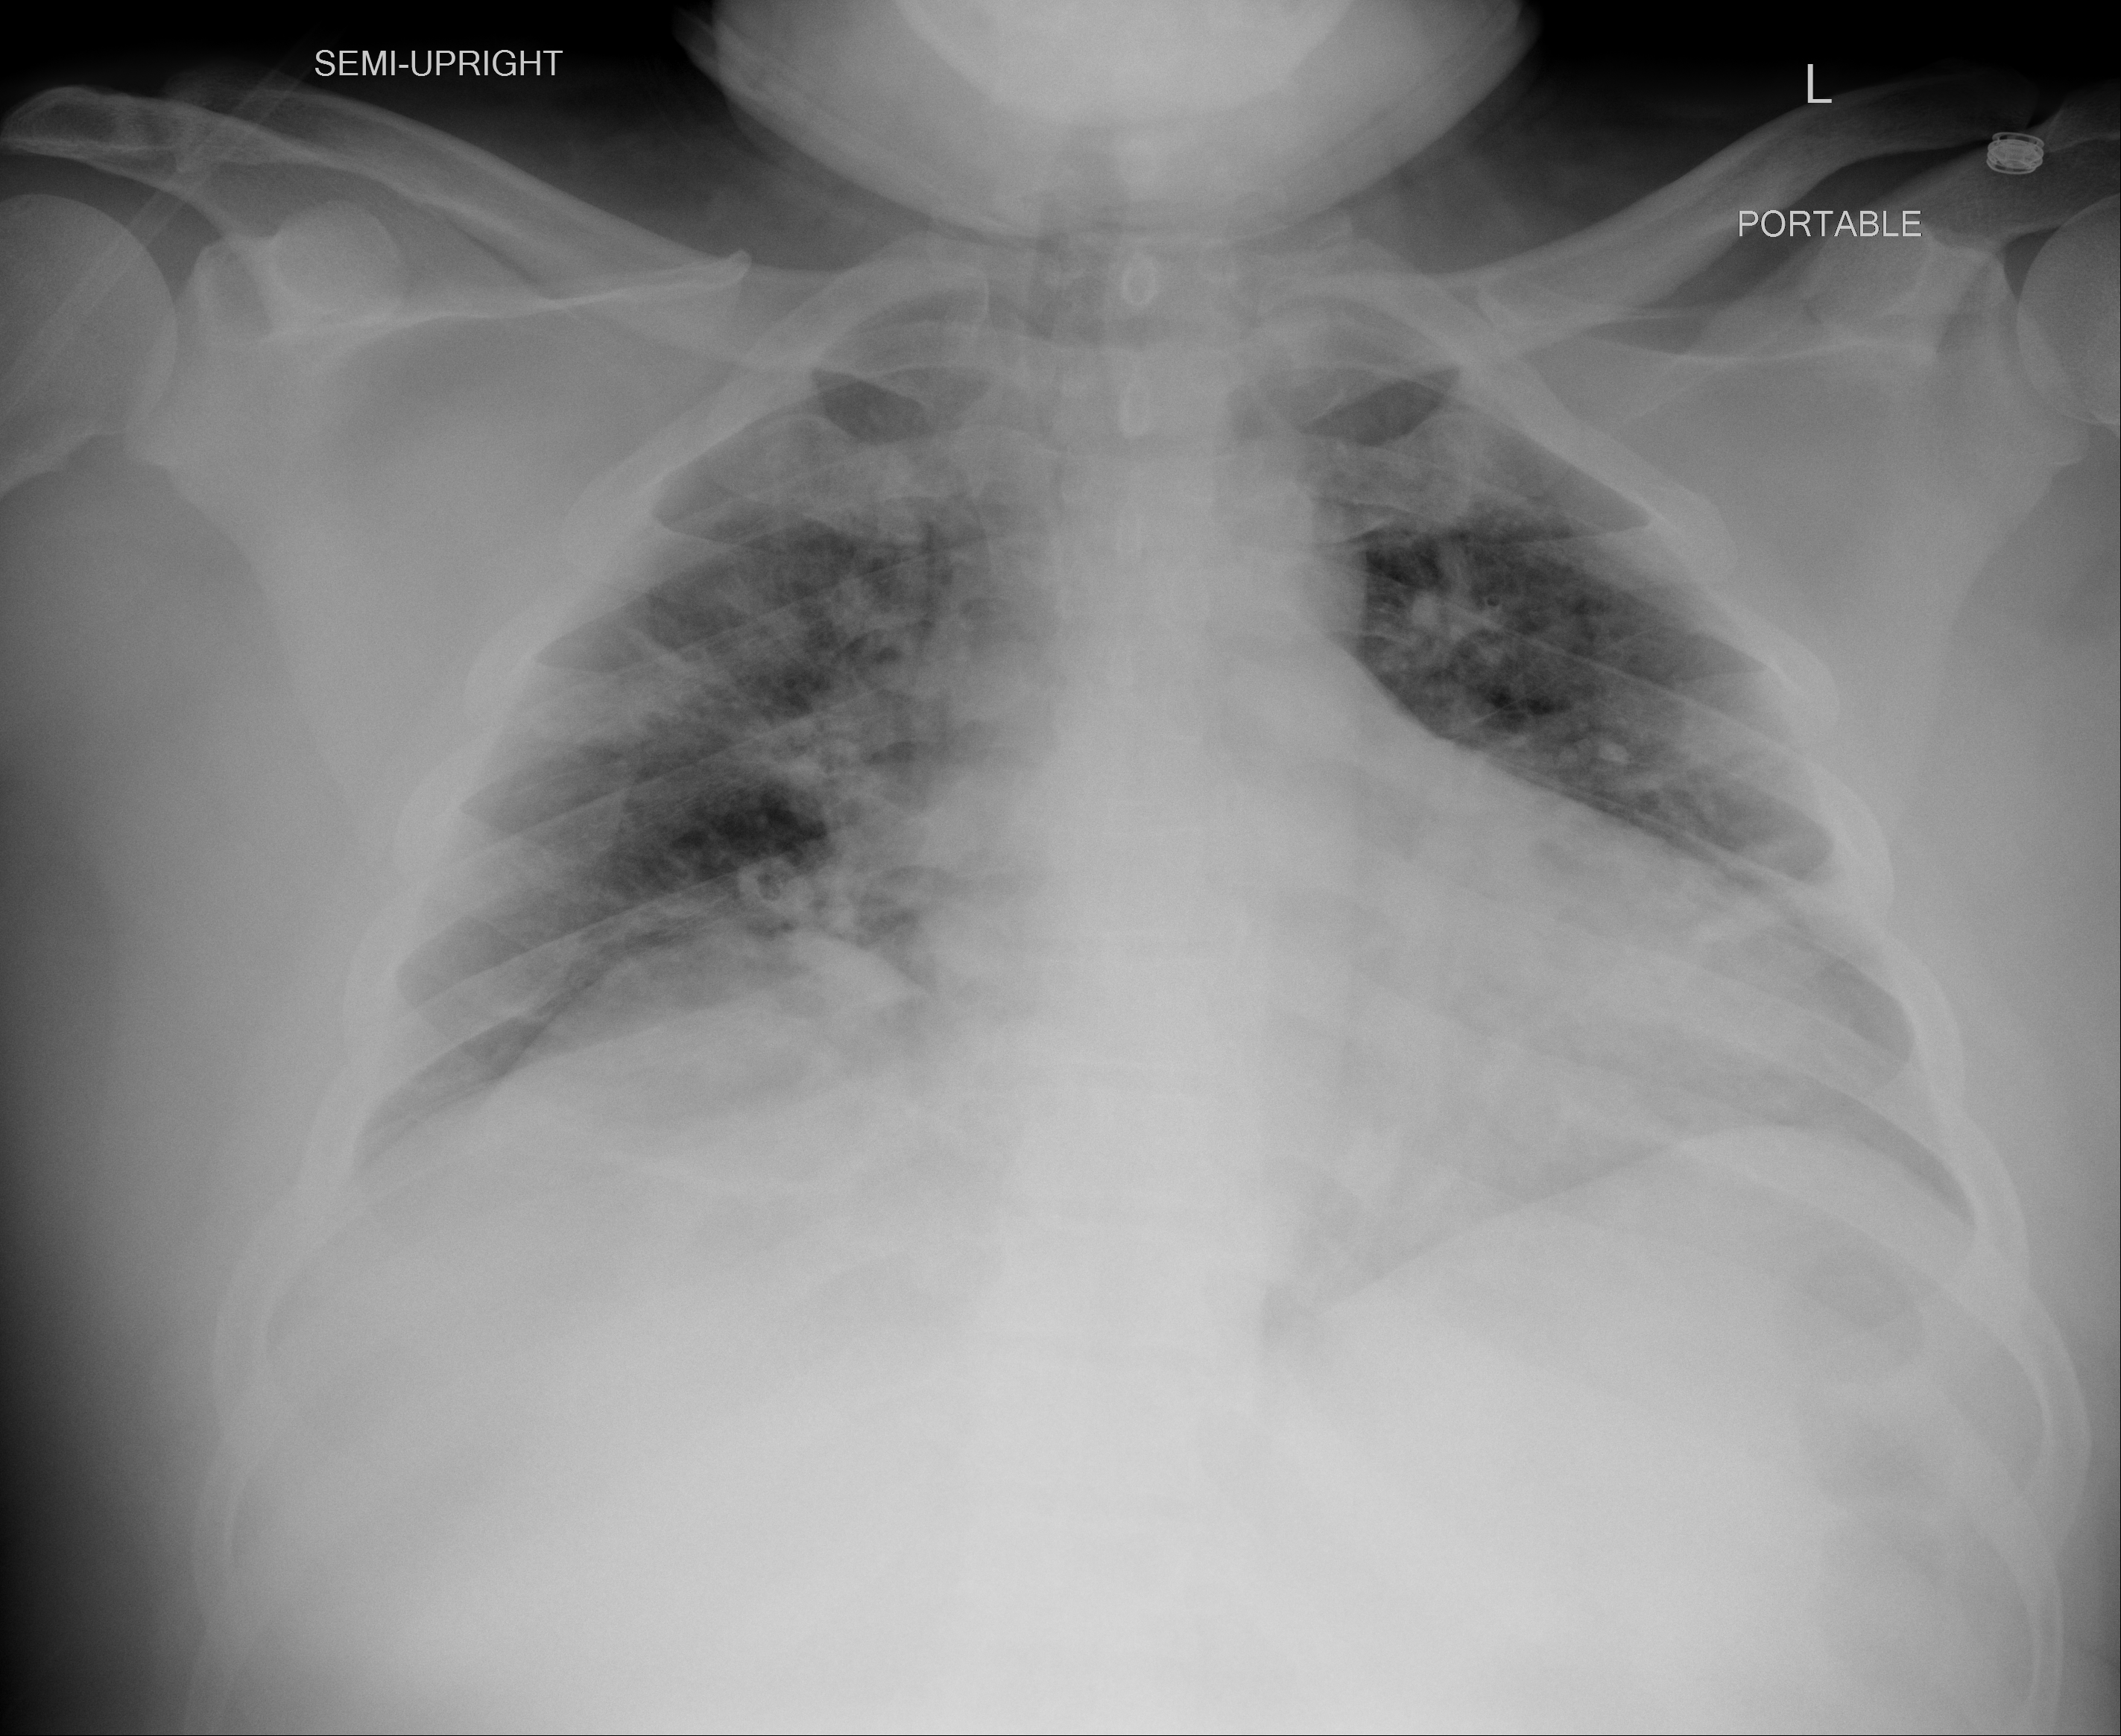
Chest X-ray (portable), AP projection. Male patient, age 48 years; imaged 1 day after the COVID-19 diagnosis.
Key findings recorded by the radiologist: mild bibasilar opacities and some peribronchovascular opacities in the right upper lobe.